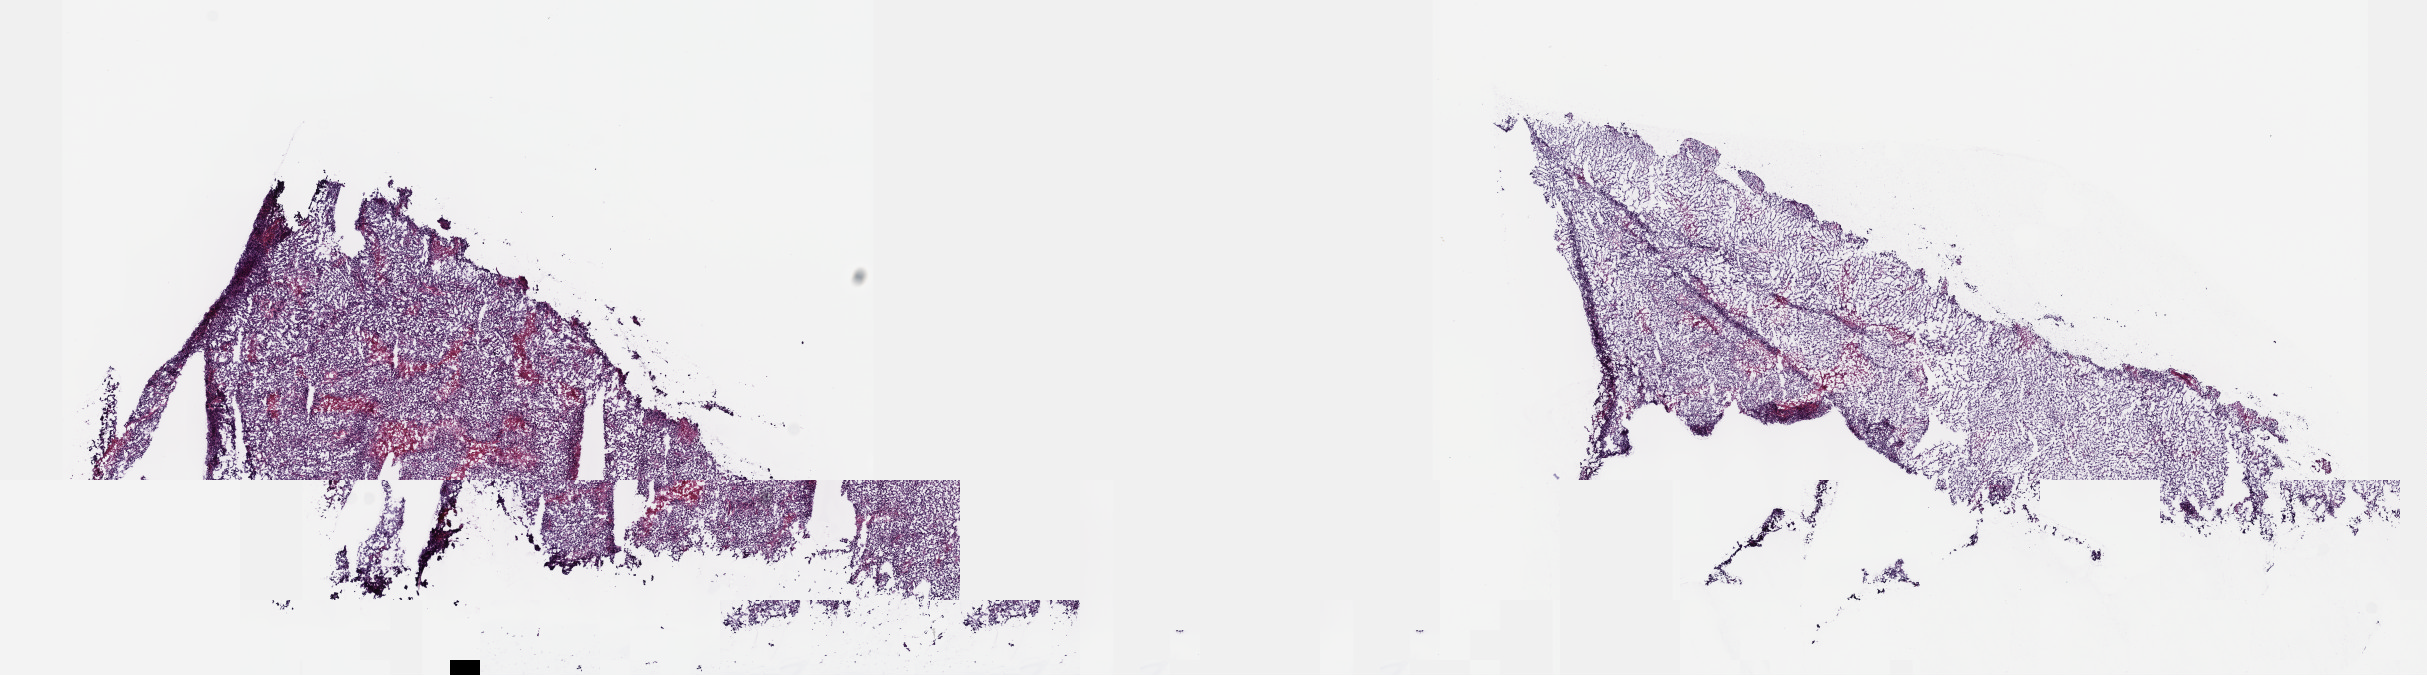
H&E whole-slide image — whole scanned area (about 19.6 x 5.5 mm, from a 40x scan) shown as a low-resolution overview, frozen section from the top of the tissue portion, sample: primary tumour, testis. Male patient; age at initial diagnosis 29 years. Pathologist review of this section (percent, as recorded): tumour cells 81%, tumour nuclei 80%, normal cells 0%, stromal cells 0%, necrosis 19%. Inflammatory infiltration, as recorded: lymphocyte infiltration 2%, monocyte infiltration 0%, neutrophil infiltration 0%.
AJCC pathologic stage: IS (6th edition). Diagnosis: Seminoma, NOS. TNM: T1 NX M0.